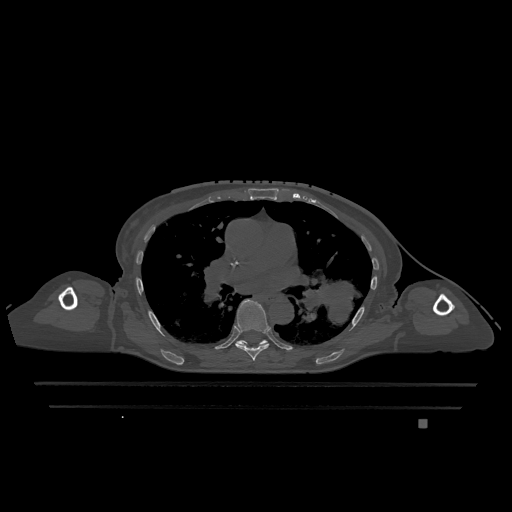
CT including the spine, one axial slice; slice 774 of 1317 in the series (ordered by position); bone window (W 1800 / L 400 HU); 512 × 512 image matrix, field of view 500 × 500 mm. Patient: female, 74 years. From the clinical record (not read from this slice): primary cancer: lung; vertebrae with lytic lesions (as recorded): T1, T4, T5, T6, L4, L5.
Outlined on this slice (semi-automatic segmentation, software-assisted and operator-edited):
- T6 vertebra: bounding box <235,300,271,361> (left, top, right, bottom; pixels)
- T7 vertebra: <237,340,268,345>